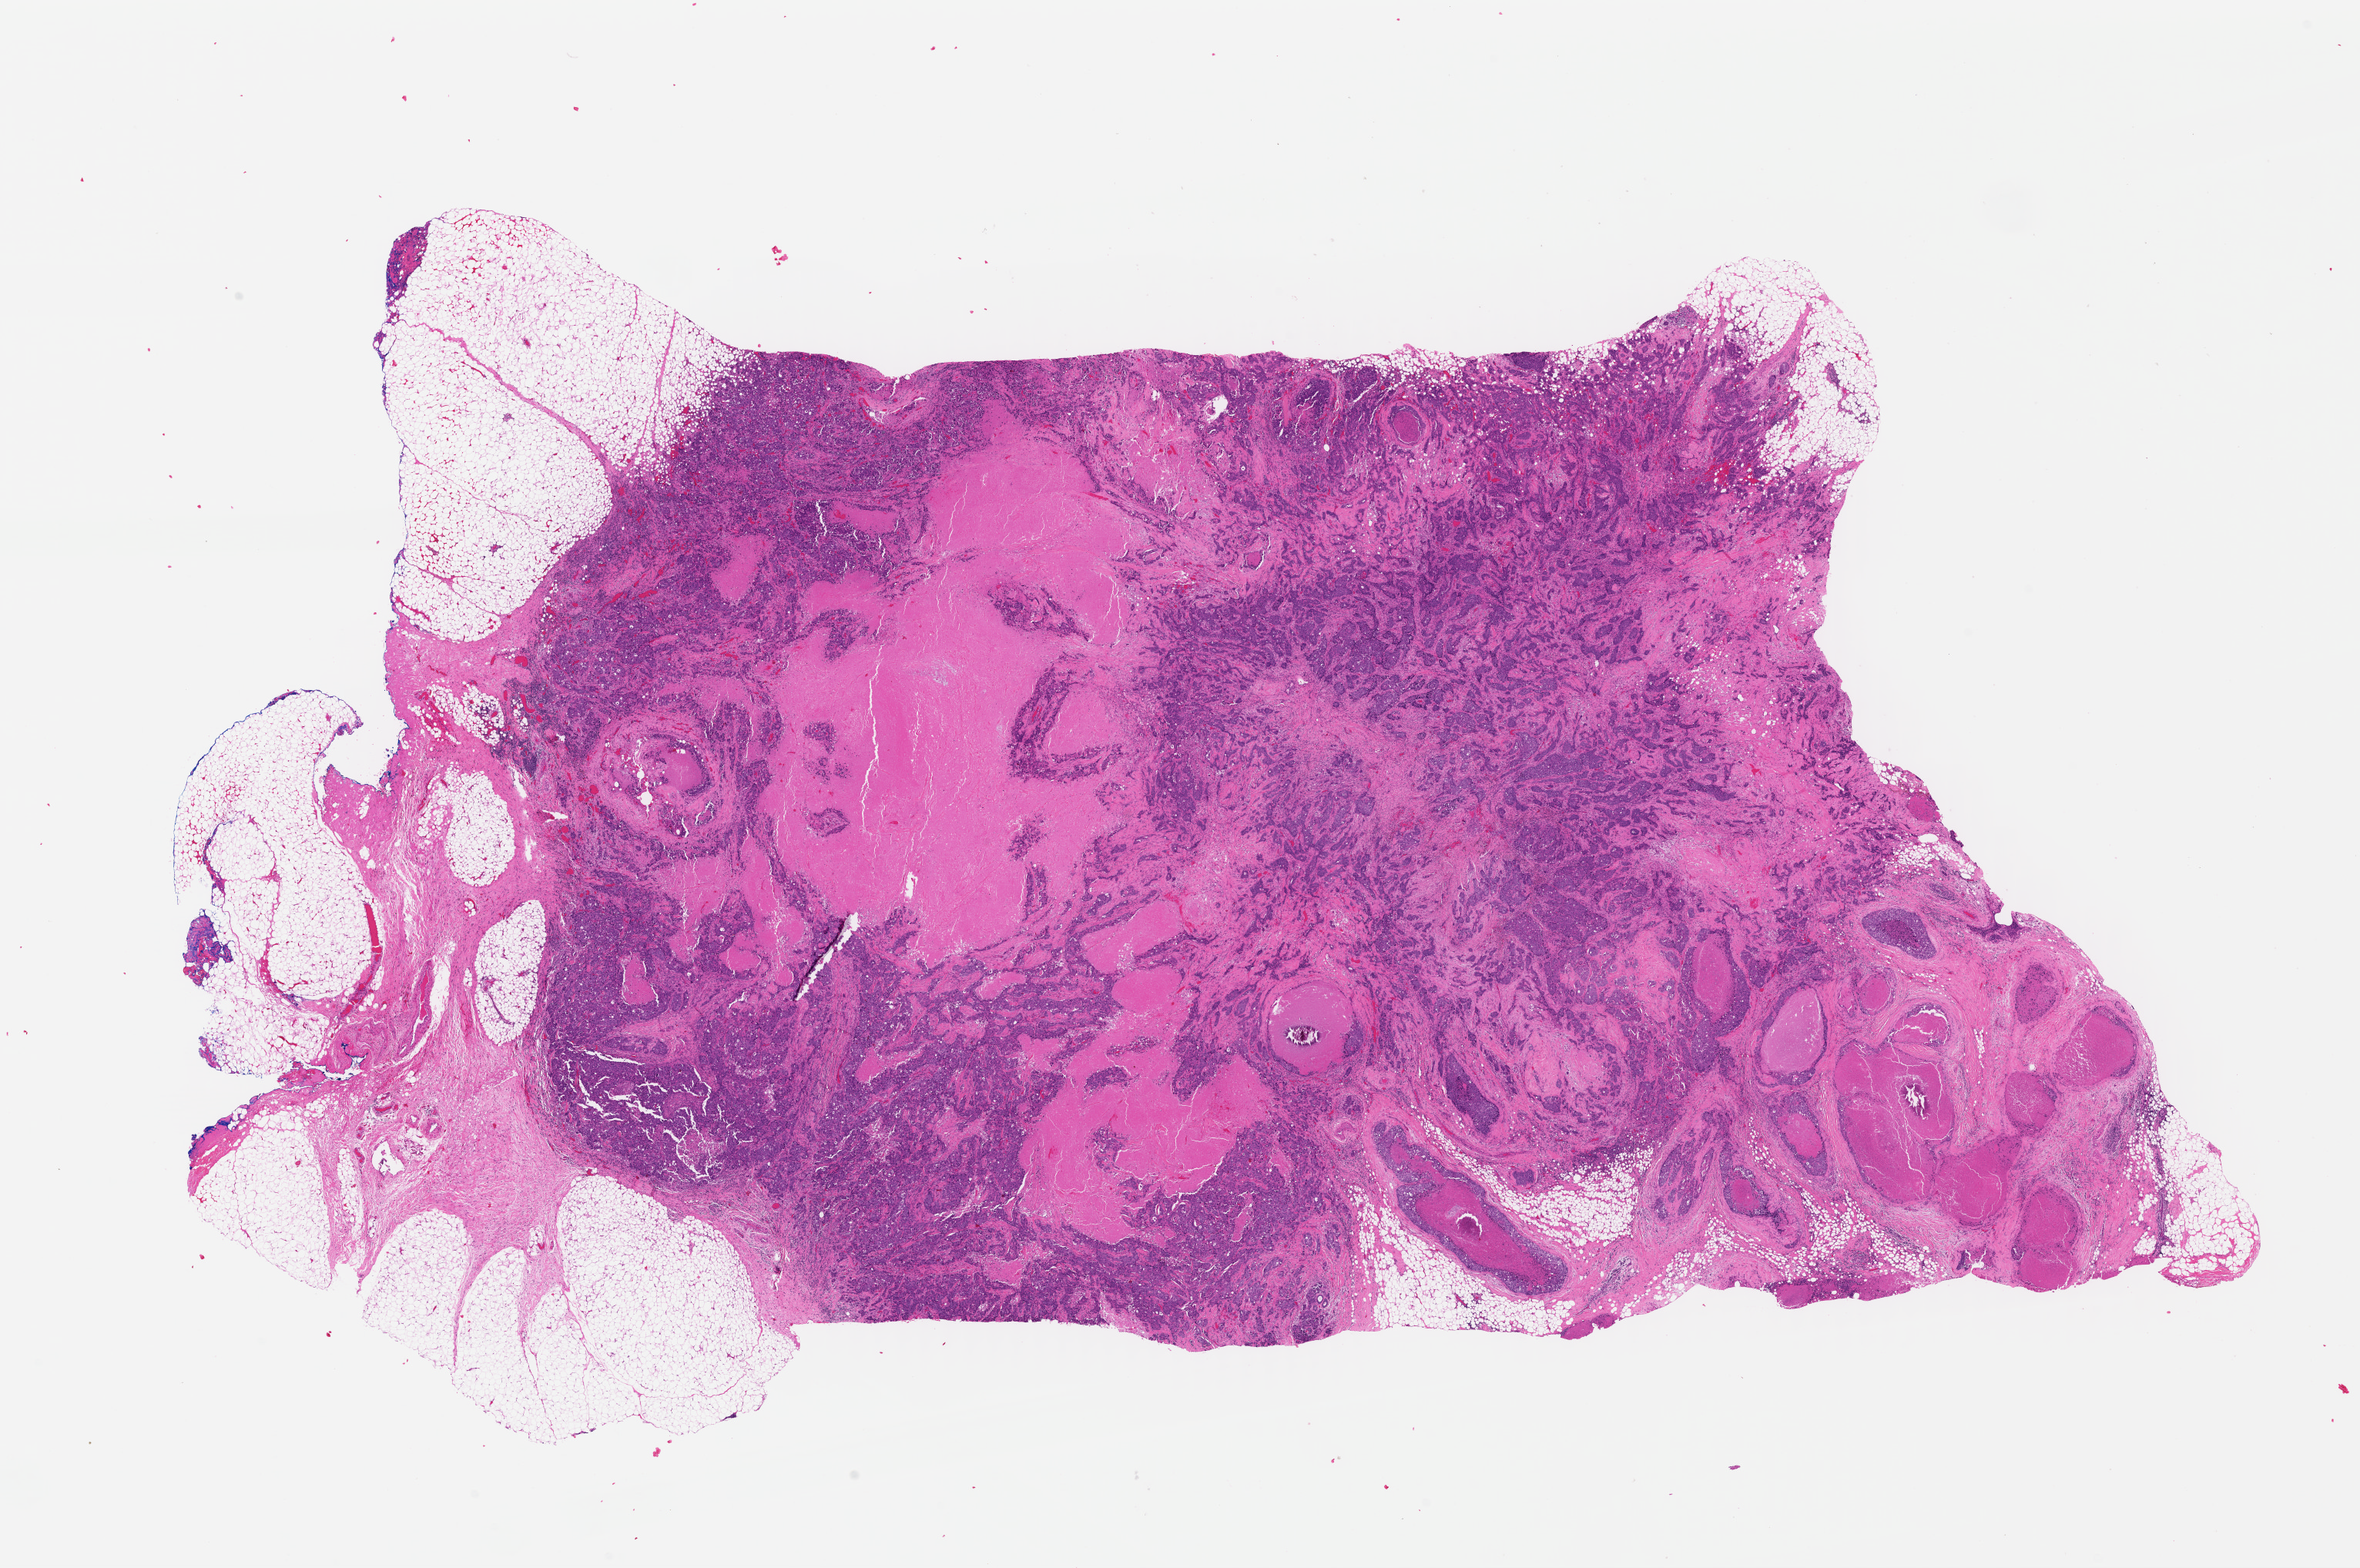
H&E whole-slide image — shown as a low-resolution overview of the whole scanned area (about 24.1 x 16.0 mm, acquisition: 40x scan), formalin-fixed paraffin-embedded (FFPE) diagnostic section, sample: primary tumour, breast. Female patient; age at initial diagnosis 49 years.
- pathologic diagnosis: Infiltrating duct carcinoma, NOS
- AJCC pathologic stage: IIB (7th edition)
- lymph nodes positive (case pathology): 3 of 16 examined